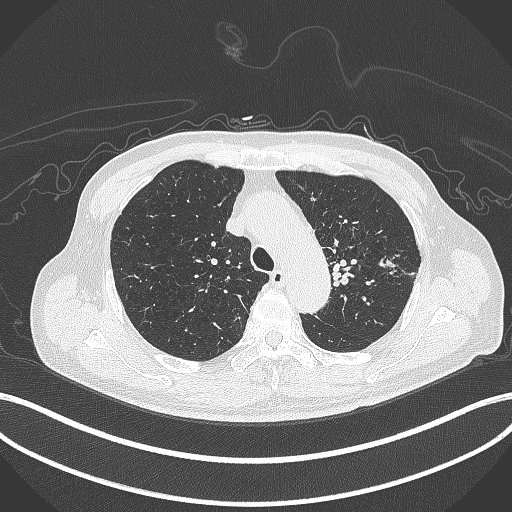
Chest CT, one axial slice; slice 328 of 417 in the series (ordered by position); reconstruction kernel B70f; lung window (W 1500 / L -600 HU); 512 × 512 image matrix, field of view 400 × 400 mm. Male patient, age 77 years. From the clinical record (not read from this slice): clinical TNM (as recorded): T3 N1 M0.
Outlined on this slice (bounding box drawn by a radiologist):
- lung tumour (recorded histology: adenocarcinoma): bounding box (x1, y1, x2, y2) in pixels: (378, 253, 394, 273)